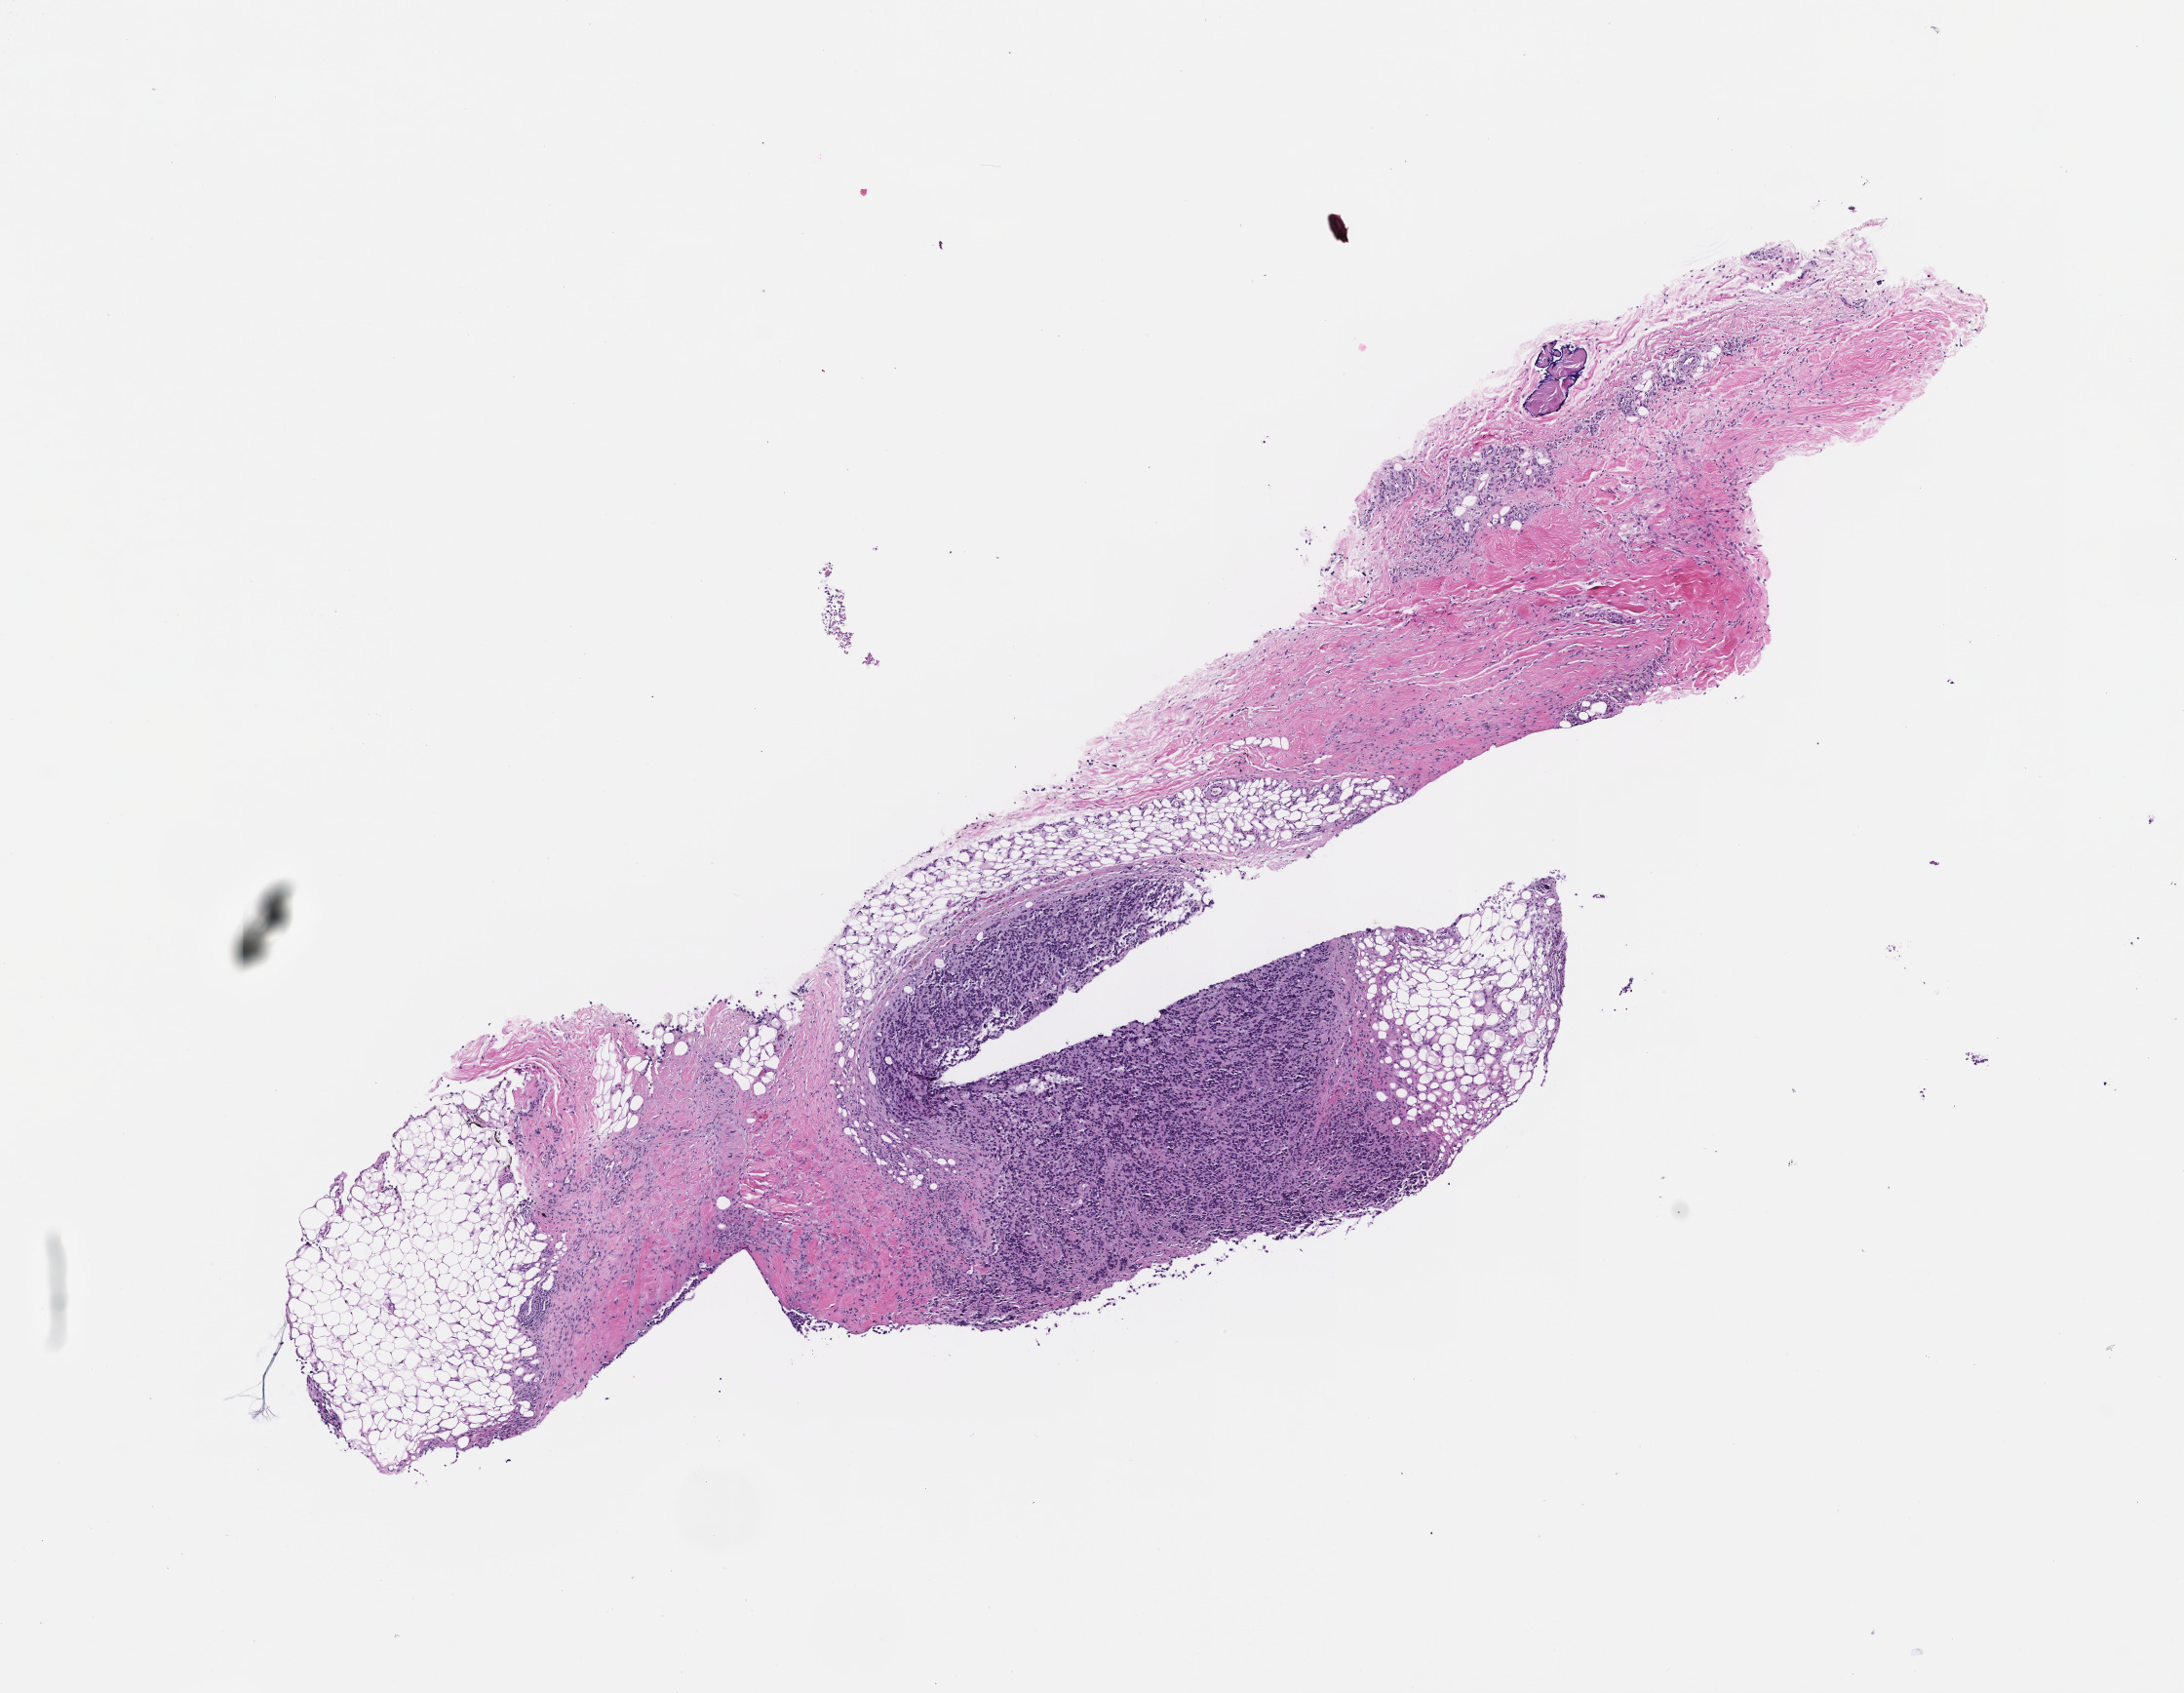
Whole-slide image, haematoxylin and eosin stain, whole scanned area (about 9.0 x 7.0 mm) shown as a low-resolution overview, FFPE section, specimen time point: collected at baseline (before treatment). Patient: male.
• this section: metastasis (sampled organ not recorded)
• primary diagnosis of the patient: Melanoma